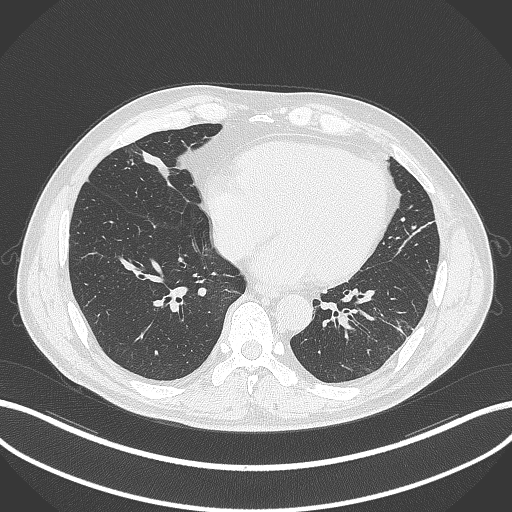
Chest CT, one axial slice. Slice 90 of 399 in the series (ordered by position). 120 kVp. Lung window (W 1500 / L -600 HU). 1 mm slice thickness. 512 × 512 image matrix, field of view 400 × 400 mm. Patient: male, 59 years. Case-level facts recorded for this patient, not image findings: clinical TNM (as recorded): T2a N1 M0.
Outlined on this slice (bounding box drawn by a radiologist):
- lung tumour (recorded histology: adenocarcinoma): bounding box [x1, y1, x2, y2] px = [135, 148, 178, 188]